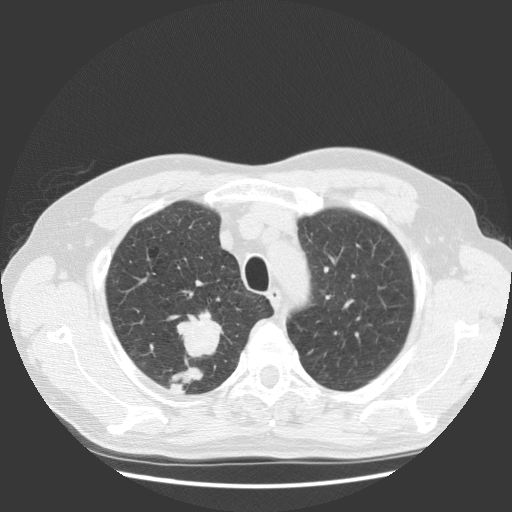
Low-dose screening chest CT, axial slice; baseline screening round; lung window (W 1500 / L -600 HU); 2.5 mm slice thickness; 140 kVp; slice 102 of 131 in the series. Male participant, aged 63 years at enrolment.
Expert reader's lesion annotation, box from (x=161, y=309) to (x=233, y=379) px. The screening reader recorded 2 non-calcified nodules or masses ≥4 mm on this exam (right upper lobe, right upper lobe); which of them this box marks is not recorded.